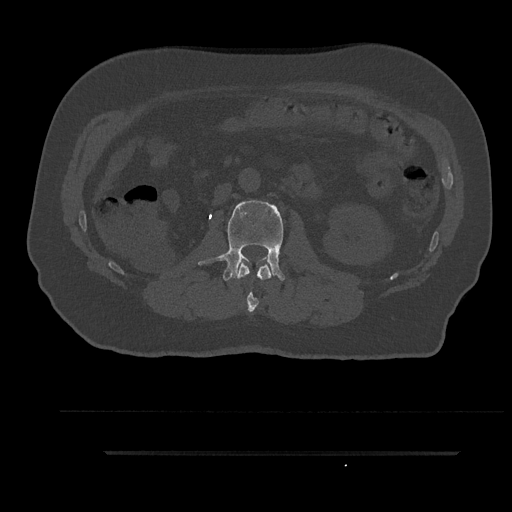
CT including the spine, one axial slice. Slice 128 of 797 in the series (ordered by position). Bone window (W 1800 / L 400 HU). 512 × 512 image matrix. Patient: male, 63 years. From the clinical record (not read from this slice): primary cancer: renal.
Structures marked on this image (semi-automatic segmentation, software-assisted and operator-edited):
- L1 vertebra: box from (x=235, y=262) to (x=274, y=313) px
- L2 vertebra: (x=198, y=200)–(x=285, y=281)